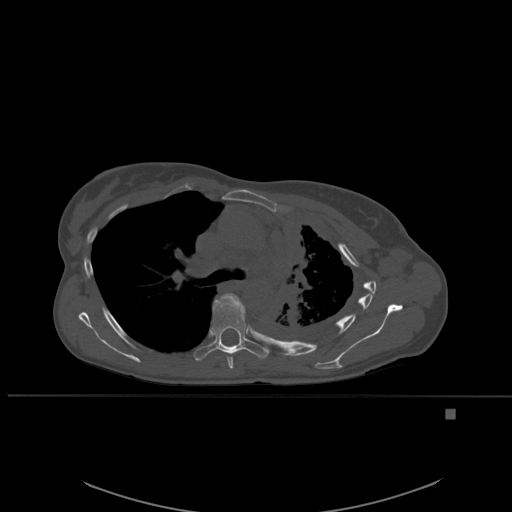
CT including the spine, one axial slice; slice 387 of 537 in the series (ordered by position); bone window (W 1800 / L 400 HU); 1.5 mm slice thickness; 512 × 512 image matrix, field of view 440 × 440 mm. Female patient, age 45 years. Case-level facts recorded for this patient, not image findings: primary cancer: lung.
Structures marked on this image (semi-automatic segmentation, software-assisted and operator-edited):
- T5 vertebra: bounding box (x1, y1, x2, y2) in pixels: (213, 293, 244, 369)
- T6 vertebra: (196, 299, 269, 361)